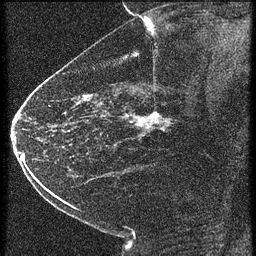
Breast MRI (dynamic contrast-enhanced), one sagittal slice; position 39 of 60 along the scan axis; 4 images stored at this slice position (order not interpretable as contrast timing); 1.5 T; TE 4.2 ms, TR 21.3 ms; 1.5 mm slice thickness; 256 × 256 image matrix. Female patient, age 43 years. Case-level facts recorded for this patient, not image findings: setting: breast cancer imaged before/during neoadjuvant chemotherapy; receptor status: HER2-positive.
Structures marked on this image (semi-automatically segmented with operator editing):
- analysis volume of interest (the breast-tissue region the enhancement analysis was run in; not a lesion): bounding box (x1, y1, x2, y2) in pixels: (122, 100, 187, 151)
- tumour enhancement mask (voxels above the 90 % enhancement threshold inside the analysis volume of interest): (132, 114, 167, 129)